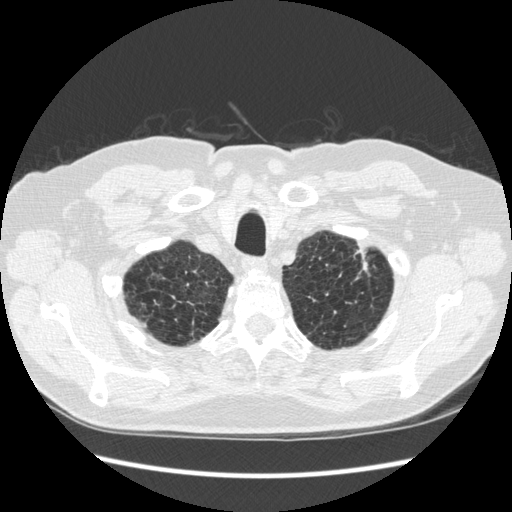
Chest CT (low-dose screening protocol), one axial image, third screening round (two years after baseline), lung window (W 1500 / L -600 HU), 1.25 mm slice thickness, standard (soft-tissue) reconstruction kernel (STANDARD), slice 28 of 267 in the series. Male participant, aged 70 years at enrolment. Former smoker at enrolment.
Lesion marked by an expert reader, bounding box <324,235,381,302> (left, top, right, bottom; pixels). The screening reader recorded 2 non-calcified nodules or masses ≥4 mm on this exam (left upper lobe, right lower lobe); which of them this box marks is not recorded. Participant outcome: lung cancer diagnosed 92 days after this screen — squamous cell carcinoma, NOS, left upper lobe, moderately differentiated (G2), stage IA (AJCC 6th edition), 18 mm at pathology.